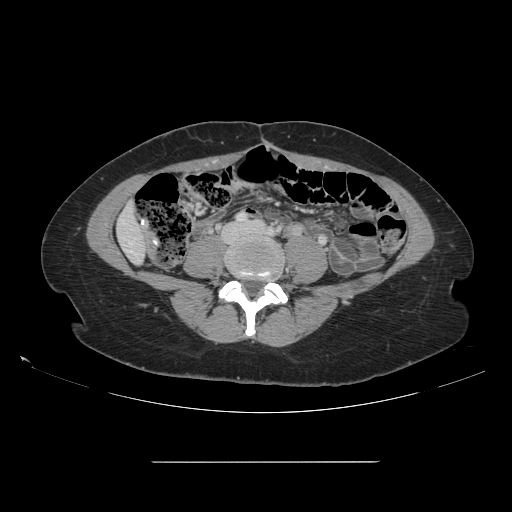
Contrast-enhanced abdominal CT, one axial slice; position 14 of 151 along the scan axis; 120 kVp; soft-tissue window (W 400 / L 40 HU); 2.5 mm slice thickness; 512 × 512 image matrix. Female patient, age 46 years. From the clinical record (not read from this slice): diagnosis: colorectal cancer liver metastases, imaged before liver resection; multiple liver metastases: yes; largest metastasis: 3 cm; disease in both lobes: yes.
Outlined on this slice (manually delineated by an expert):
- liver: box from (x=118, y=206) to (x=147, y=263) px
- planned liver remnant (the part of the liver to remain after resection): (x=118, y=206)–(x=147, y=262)